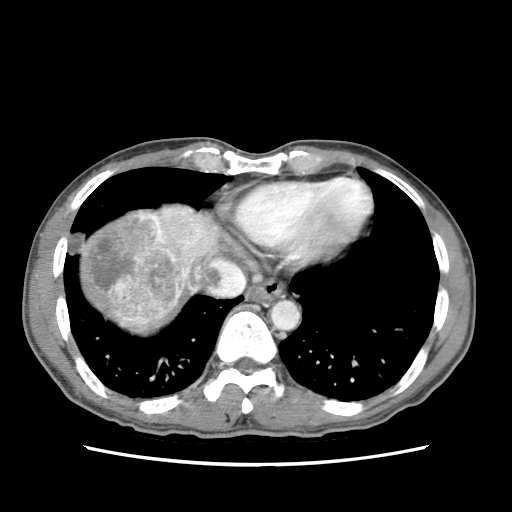
Contrast-enhanced abdominal CT (liver protocol), one axial slice. Position 68 of 79 along the scan axis. Reconstruction kernel STANDARD. 120 kVp. Soft-tissue window (W 400 / L 40 HU). 2.5 mm slice thickness. 512 × 512 image matrix, field of view 320 × 320 mm. Case-level facts recorded for this patient, not image findings: diagnosis: hepatocellular carcinoma (patient treated with transarterial chemoembolisation; whether this scan precedes or follows treatment is not stated here); TNM stage (as recorded): Stage-IIIB; Child-Pugh class: A; tumour differentiation: moderately differentiated; tumour nodularity: multinodular.
Structures marked on this image (semi-automatically segmented with operator editing):
- liver parenchyma outside the tumour (the mass and vessels are separate outlines, so this box may not span the whole liver): bounding box <72,200,242,336> (left, top, right, bottom; pixels)
- mass: <82,208,191,330>
- liver vessels: <163,204,198,247>